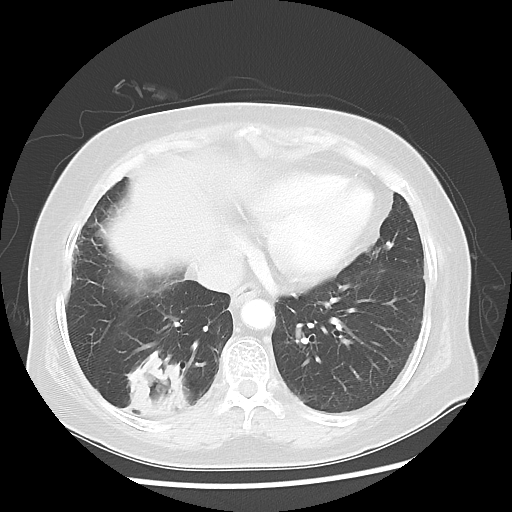
Chest CT, one axial slice; slice 18 of 56 in the series (ordered by position); lung window (W 1500 / L -600 HU); 5 mm slice thickness; 512 × 512 image matrix, field of view 360 × 360 mm. Patient: female, 64 years. Case-level facts recorded for this patient, not image findings: clinical TNM (as recorded): Tis N0 M0.
Outlined on this slice (rectangle marked by the reading radiologist):
- lung tumour (recorded histology: adenocarcinoma): bounding box <116,343,201,432> (left, top, right, bottom; pixels)